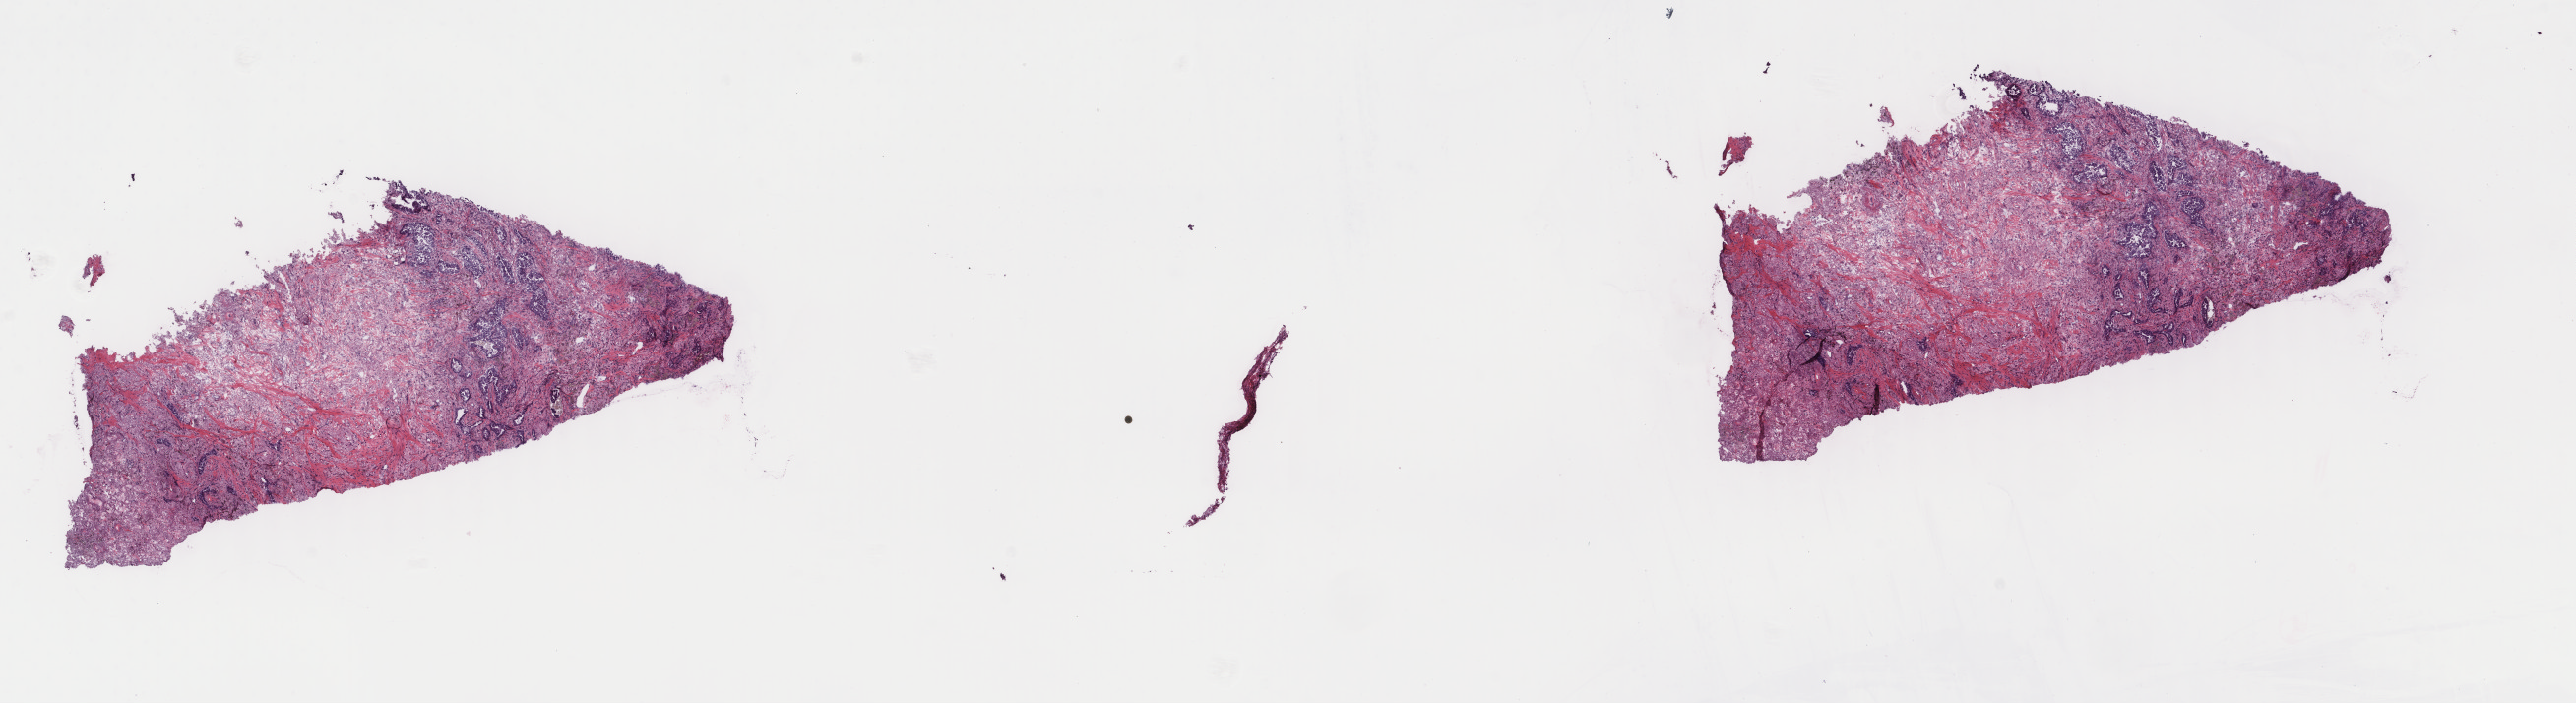
Whole-slide histology image, H&E — a low-resolution overview of the entire scanned area, about 20.8 x 5.7 mm, frozen section from the top of the tissue portion, lung, primary tumour sample. Patient: male, age at initial diagnosis 57 years. Composition of this section per pathologist review: tumour cells 85%, tumour nuclei 60%, normal cells 0%, stromal cells 15%, necrosis 0%. Infiltration values recorded for this section: lymphocyte infiltration 5%, monocyte infiltration 4%, neutrophil infiltration 0%.
* diagnosis: Adenocarcinoma, NOS (upper lobe, lung)
* laterality: left
* AJCC pathologic stage: IA